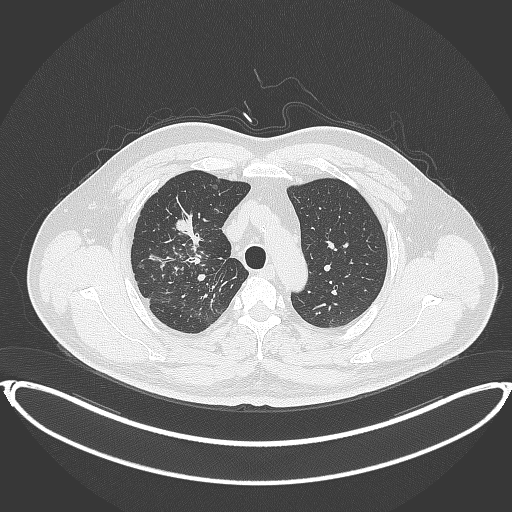
Chest CT, one axial slice; position 297 of 399 along the scan axis; reconstruction kernel B70f; 120 kVp; lung window (W 1500 / L -600 HU); 1 mm slice thickness; 512 × 512 image matrix. Patient: male, 53 years. From the clinical record (not read from this slice): clinical TNM (as recorded): T2a N0 M0.
Annotated regions visible in this slice (rectangle marked by the reading radiologist):
- lung tumour (recorded histology: adenocarcinoma): box from (x=175, y=214) to (x=191, y=239) px